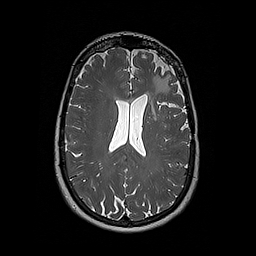
Brain MRI from a brain-tumour surgery series, one axial slice; slice 113 of 192 in the series (ordered by position); 1 mm slice thickness; 256 × 256 image matrix. From the clinical record (not read from this slice): histopathology: Oligodendroglioma; WHO grade: 2; IDH mutation: yes.
Structures marked on this image (outlined manually by an expert reader):
- tumour: bounding box (x1, y1, x2, y2) in pixels: (147, 76, 161, 117)